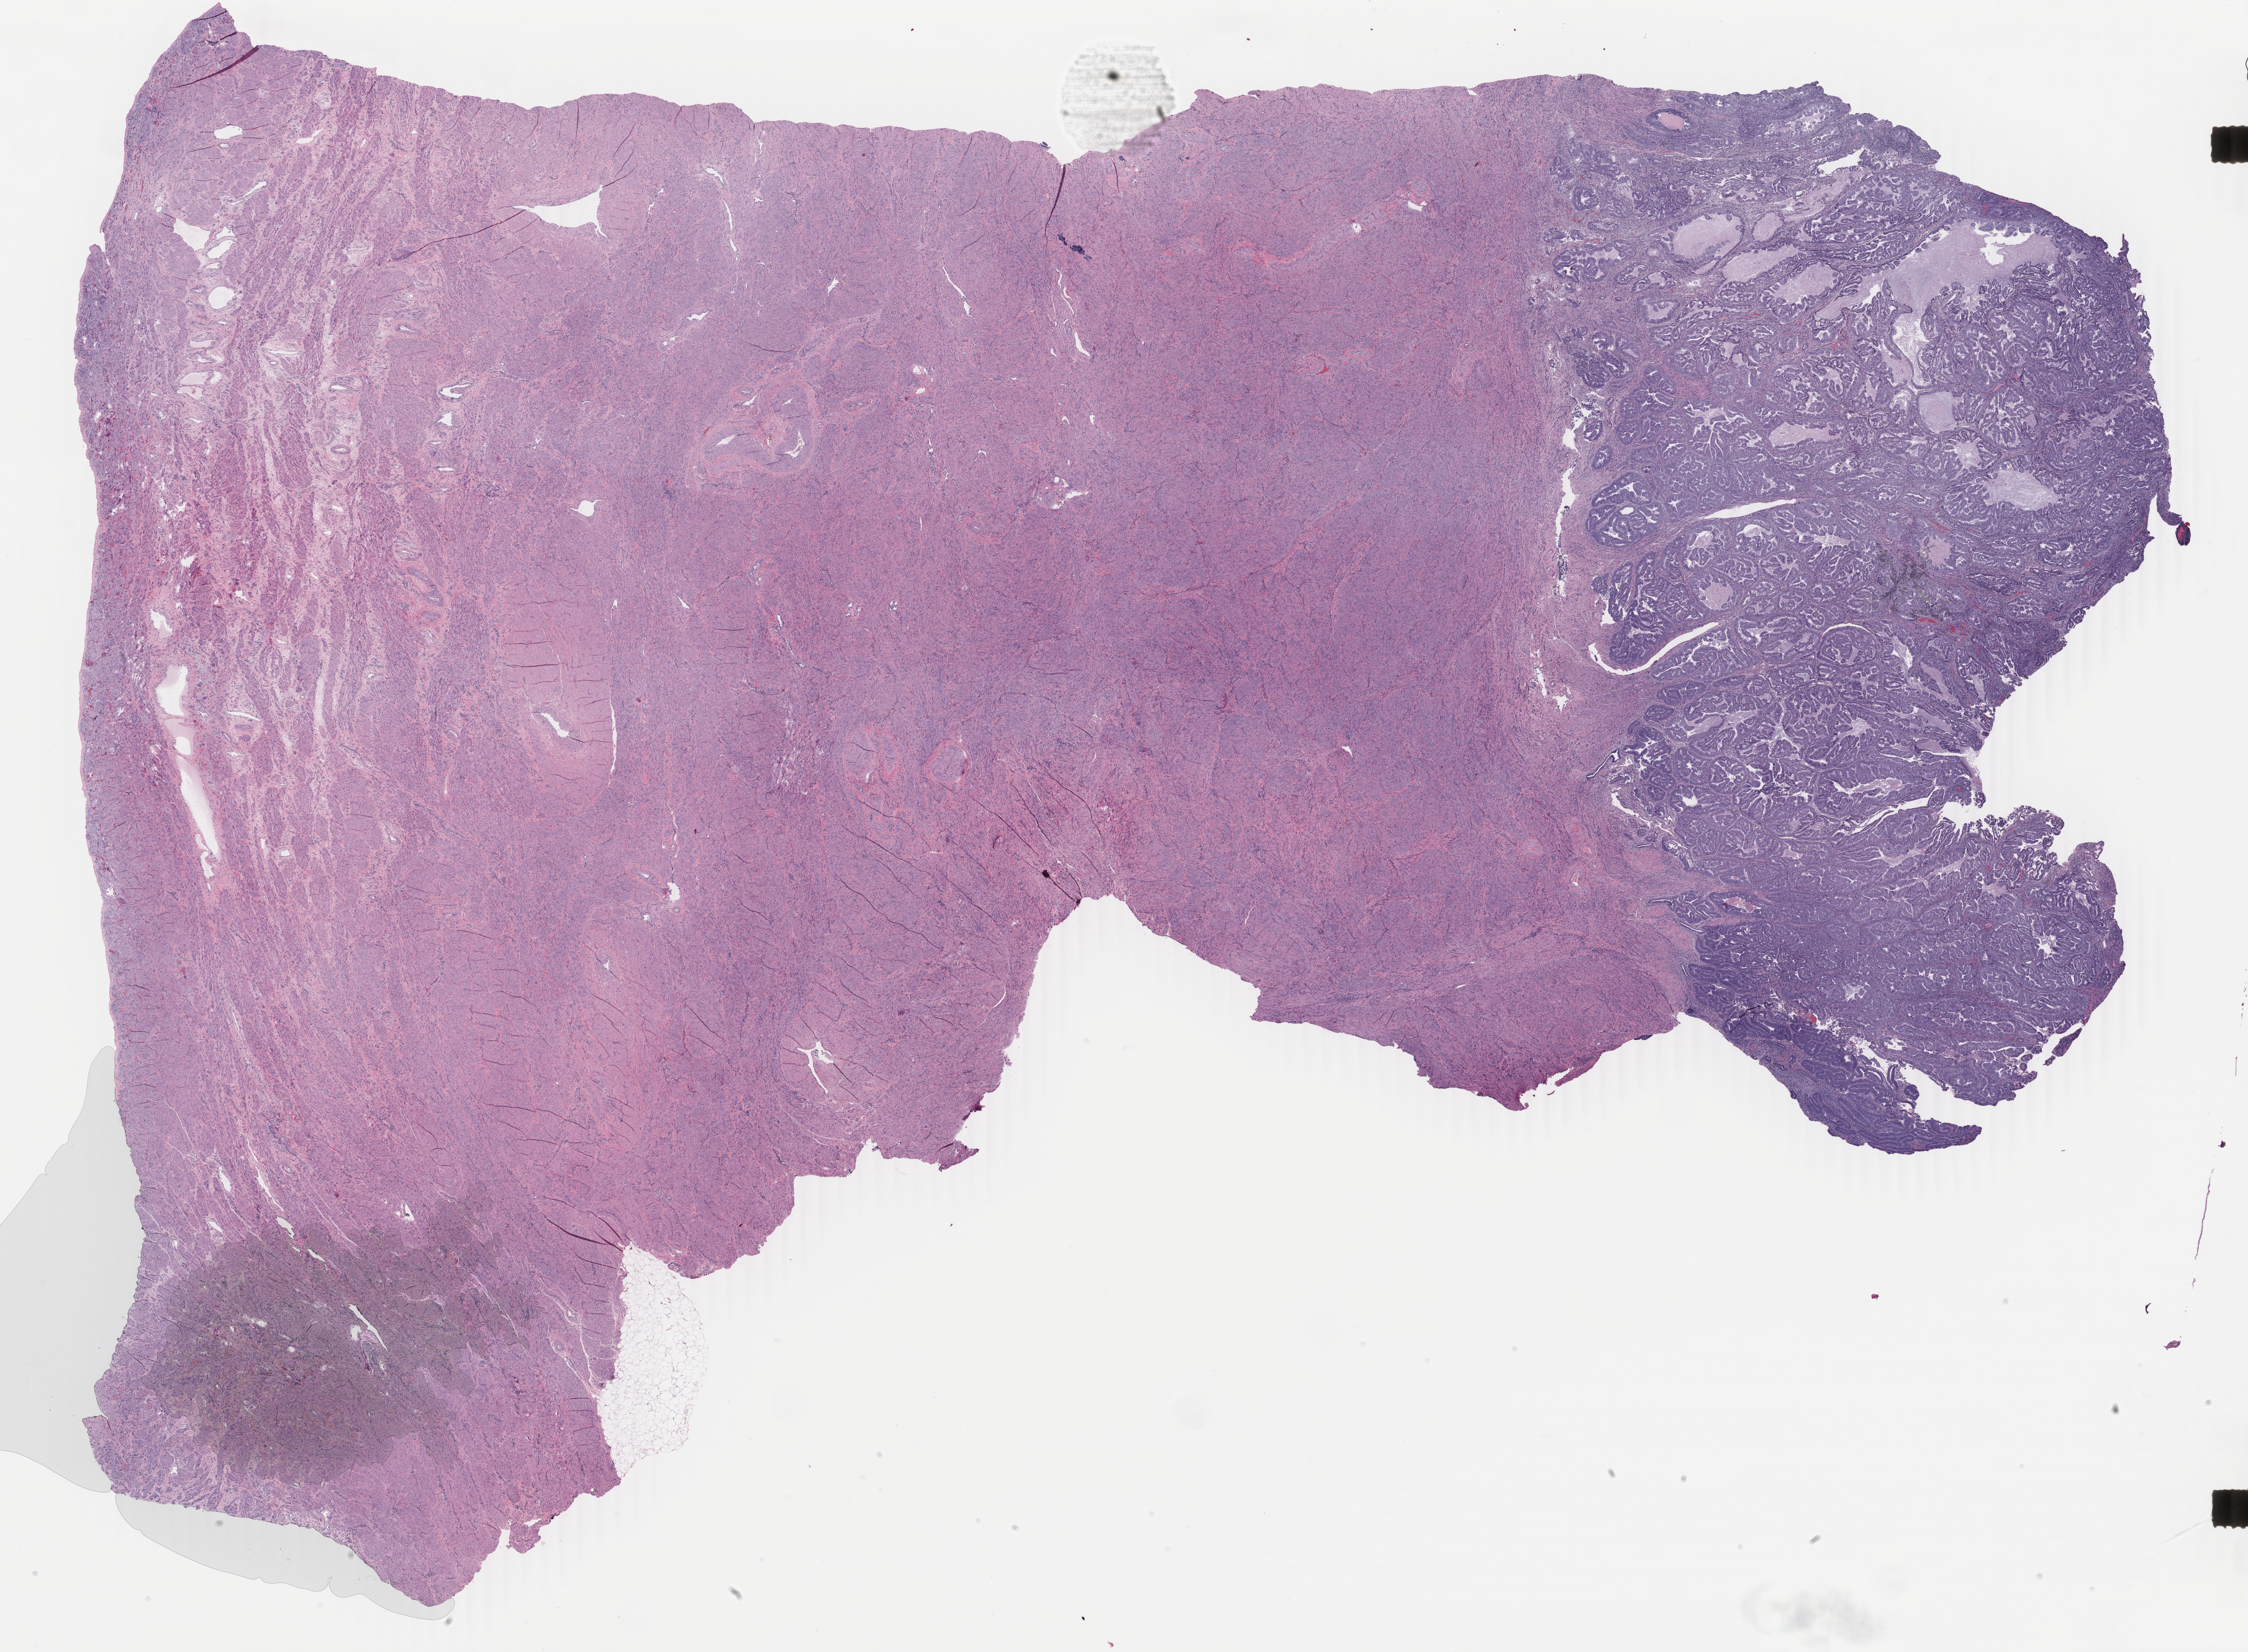
H&E whole-slide image — whole scanned area (about 28.8 x 21.2 mm, from a 40x scan) shown as a low-resolution overview, FFPE section, primary tumour sample from the uterus. Female, age 37 years at initial diagnosis. Histologic grade: G1 (well differentiated).
FIGO stage: IA. Pathologic diagnosis: Endometrioid adenocarcinoma, NOS (endometrium).